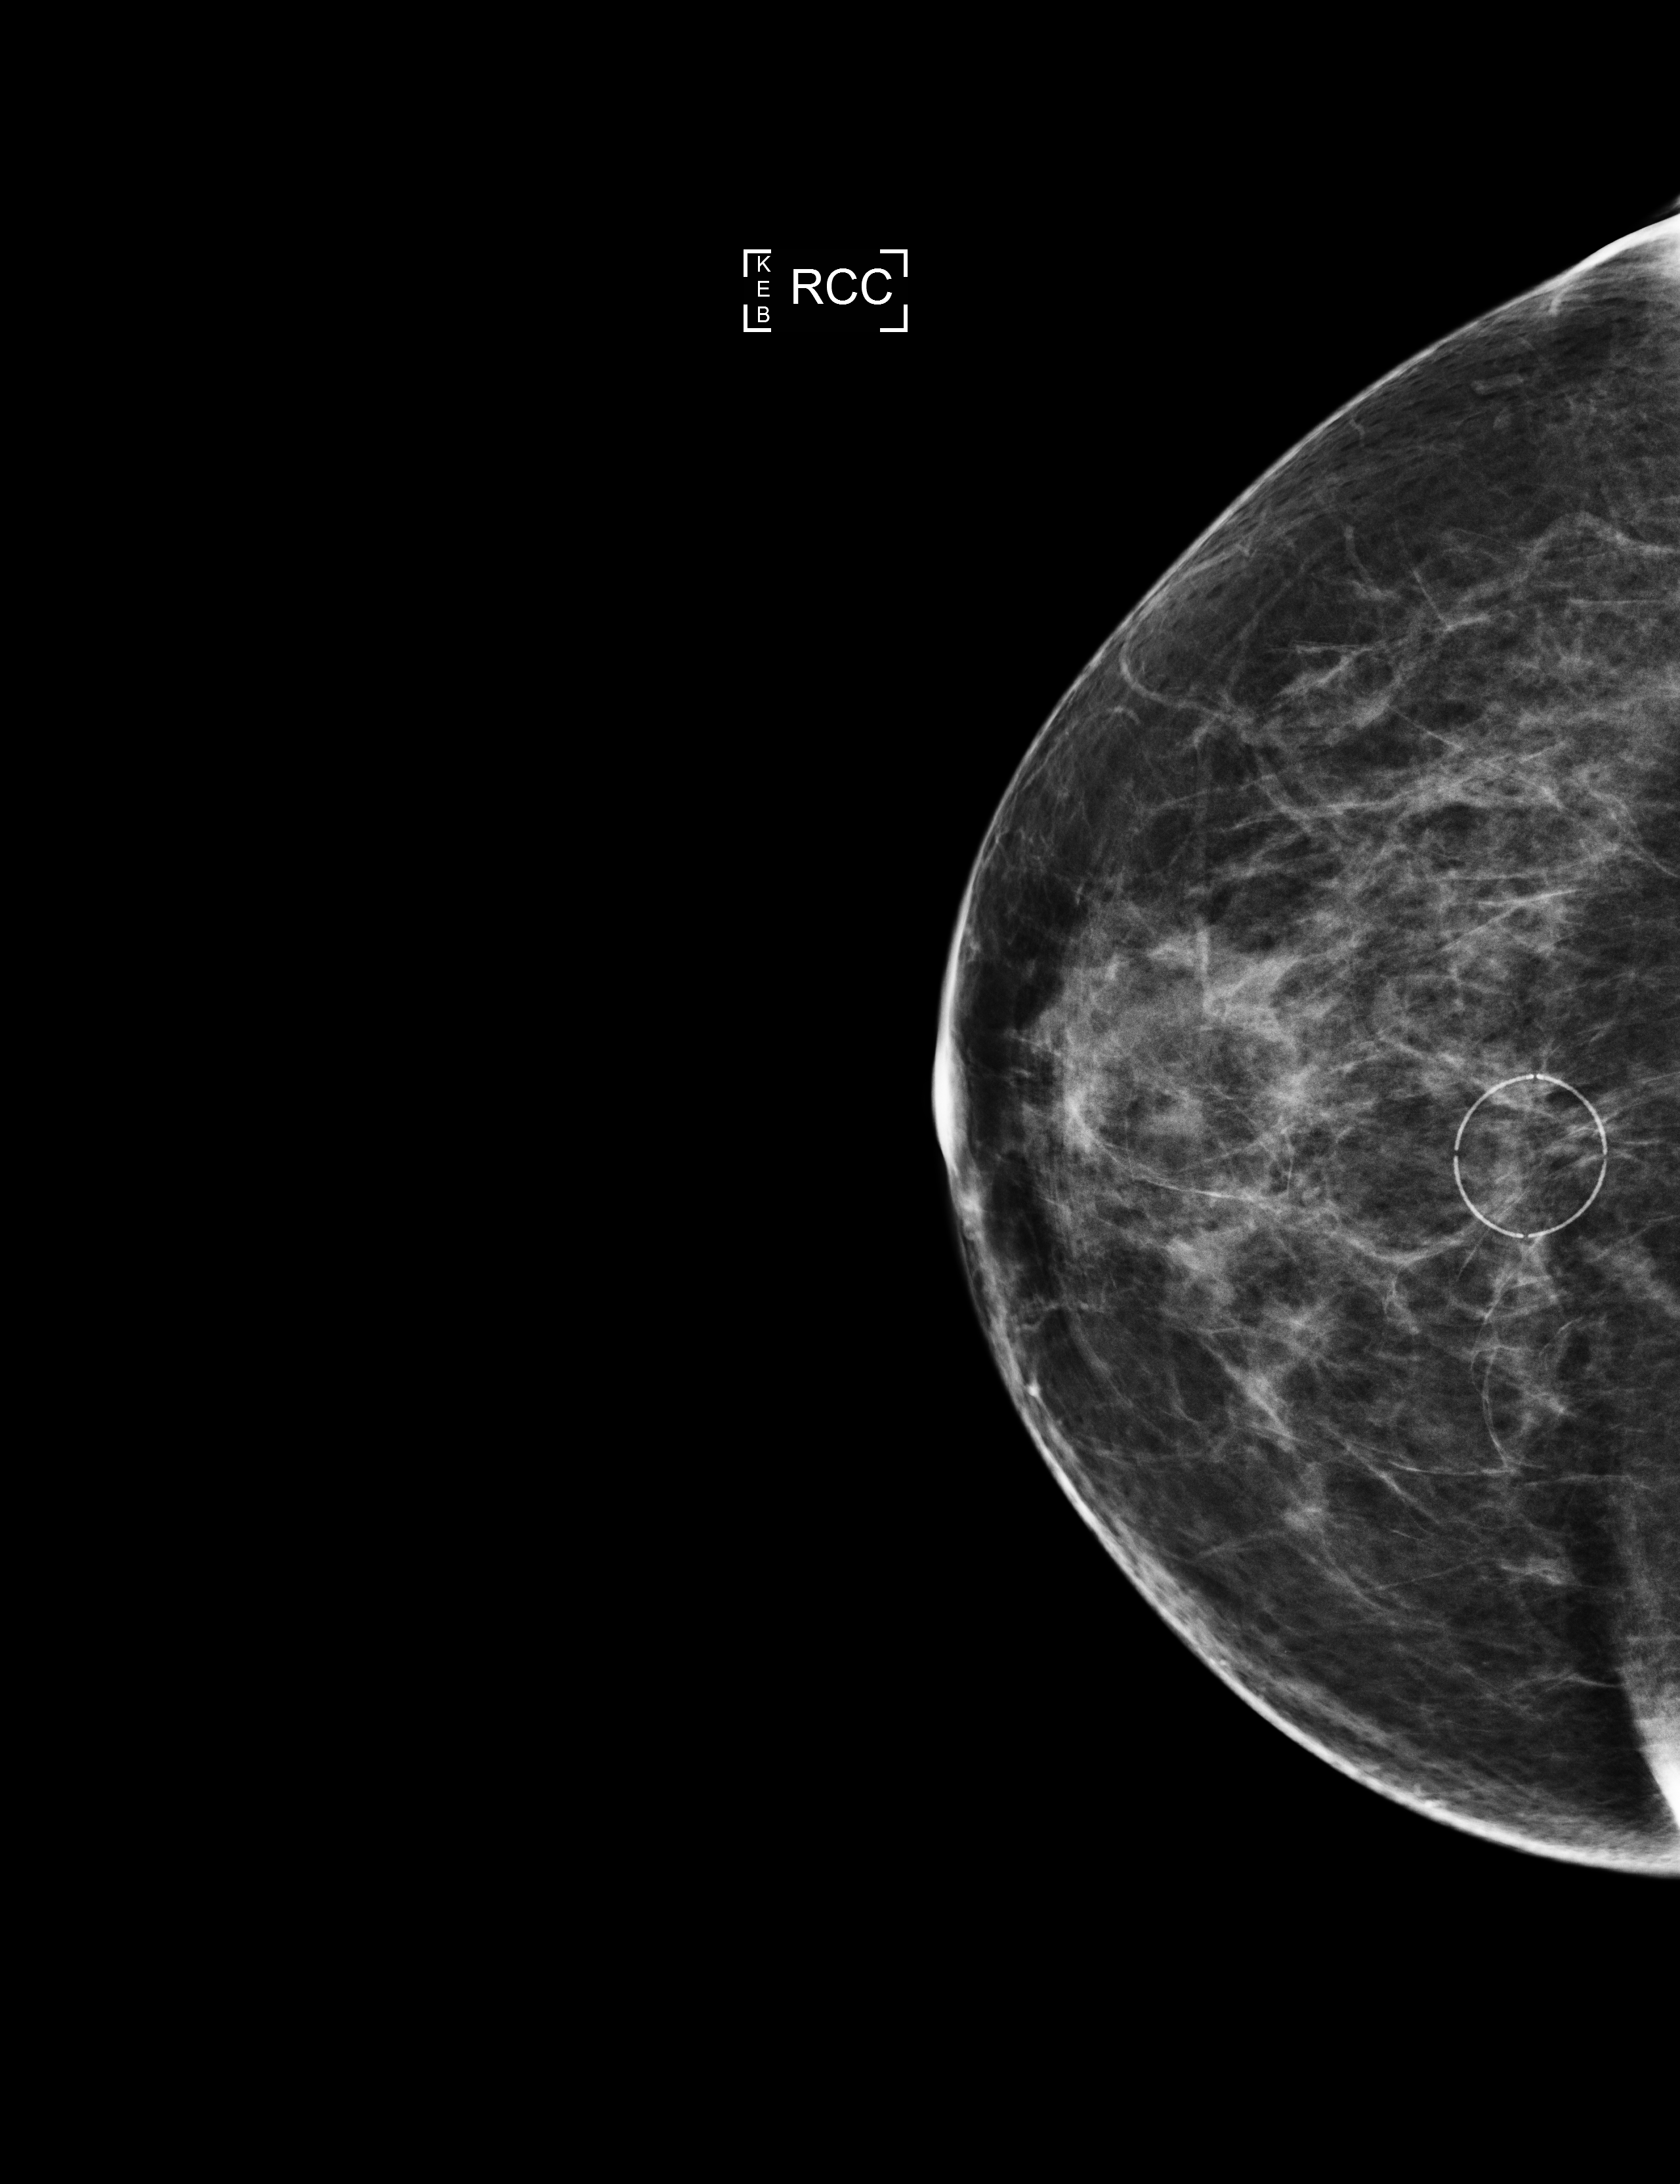
Digital mammogram (FFDM), right breast, CC view, screening examination, system: Selenia Dimensions. Female patient, age 60 years.
Breast density at the screening exam (both breasts): heterogeneously dense (BI-RADS density category c). Final BI-RADS assessment for this screening round (tomosynthesis exam, both breasts): category 1. Recall: no recall after this screen.